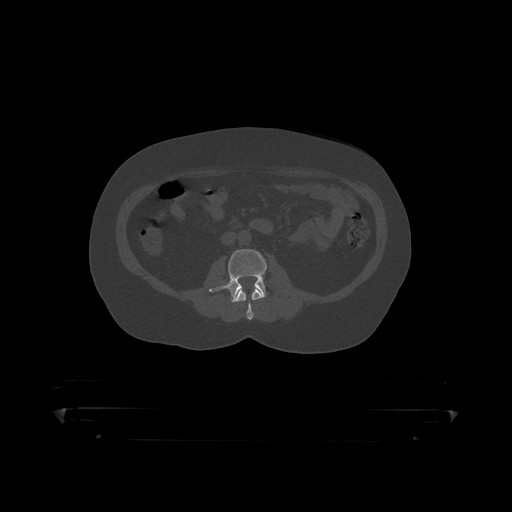
CT including the spine, one axial slice. Slice 100 of 390 in the series (ordered by position). Reconstruction kernel STANDARD. 120 kVp. Bone window (W 1800 / L 400 HU). 1.25 mm slice thickness. 512 × 512 image matrix, field of view 650 × 650 mm. Patient: male, 60 years. Case-level facts recorded for this patient, not image findings: primary cancer: prostate.
Annotated regions visible in this slice (semi-automatic segmentation, software-assisted and operator-edited):
- L2 vertebra: bounding box (x1, y1, x2, y2) in pixels: (235, 288, 264, 319)
- L3 vertebra: (209, 249, 267, 303)